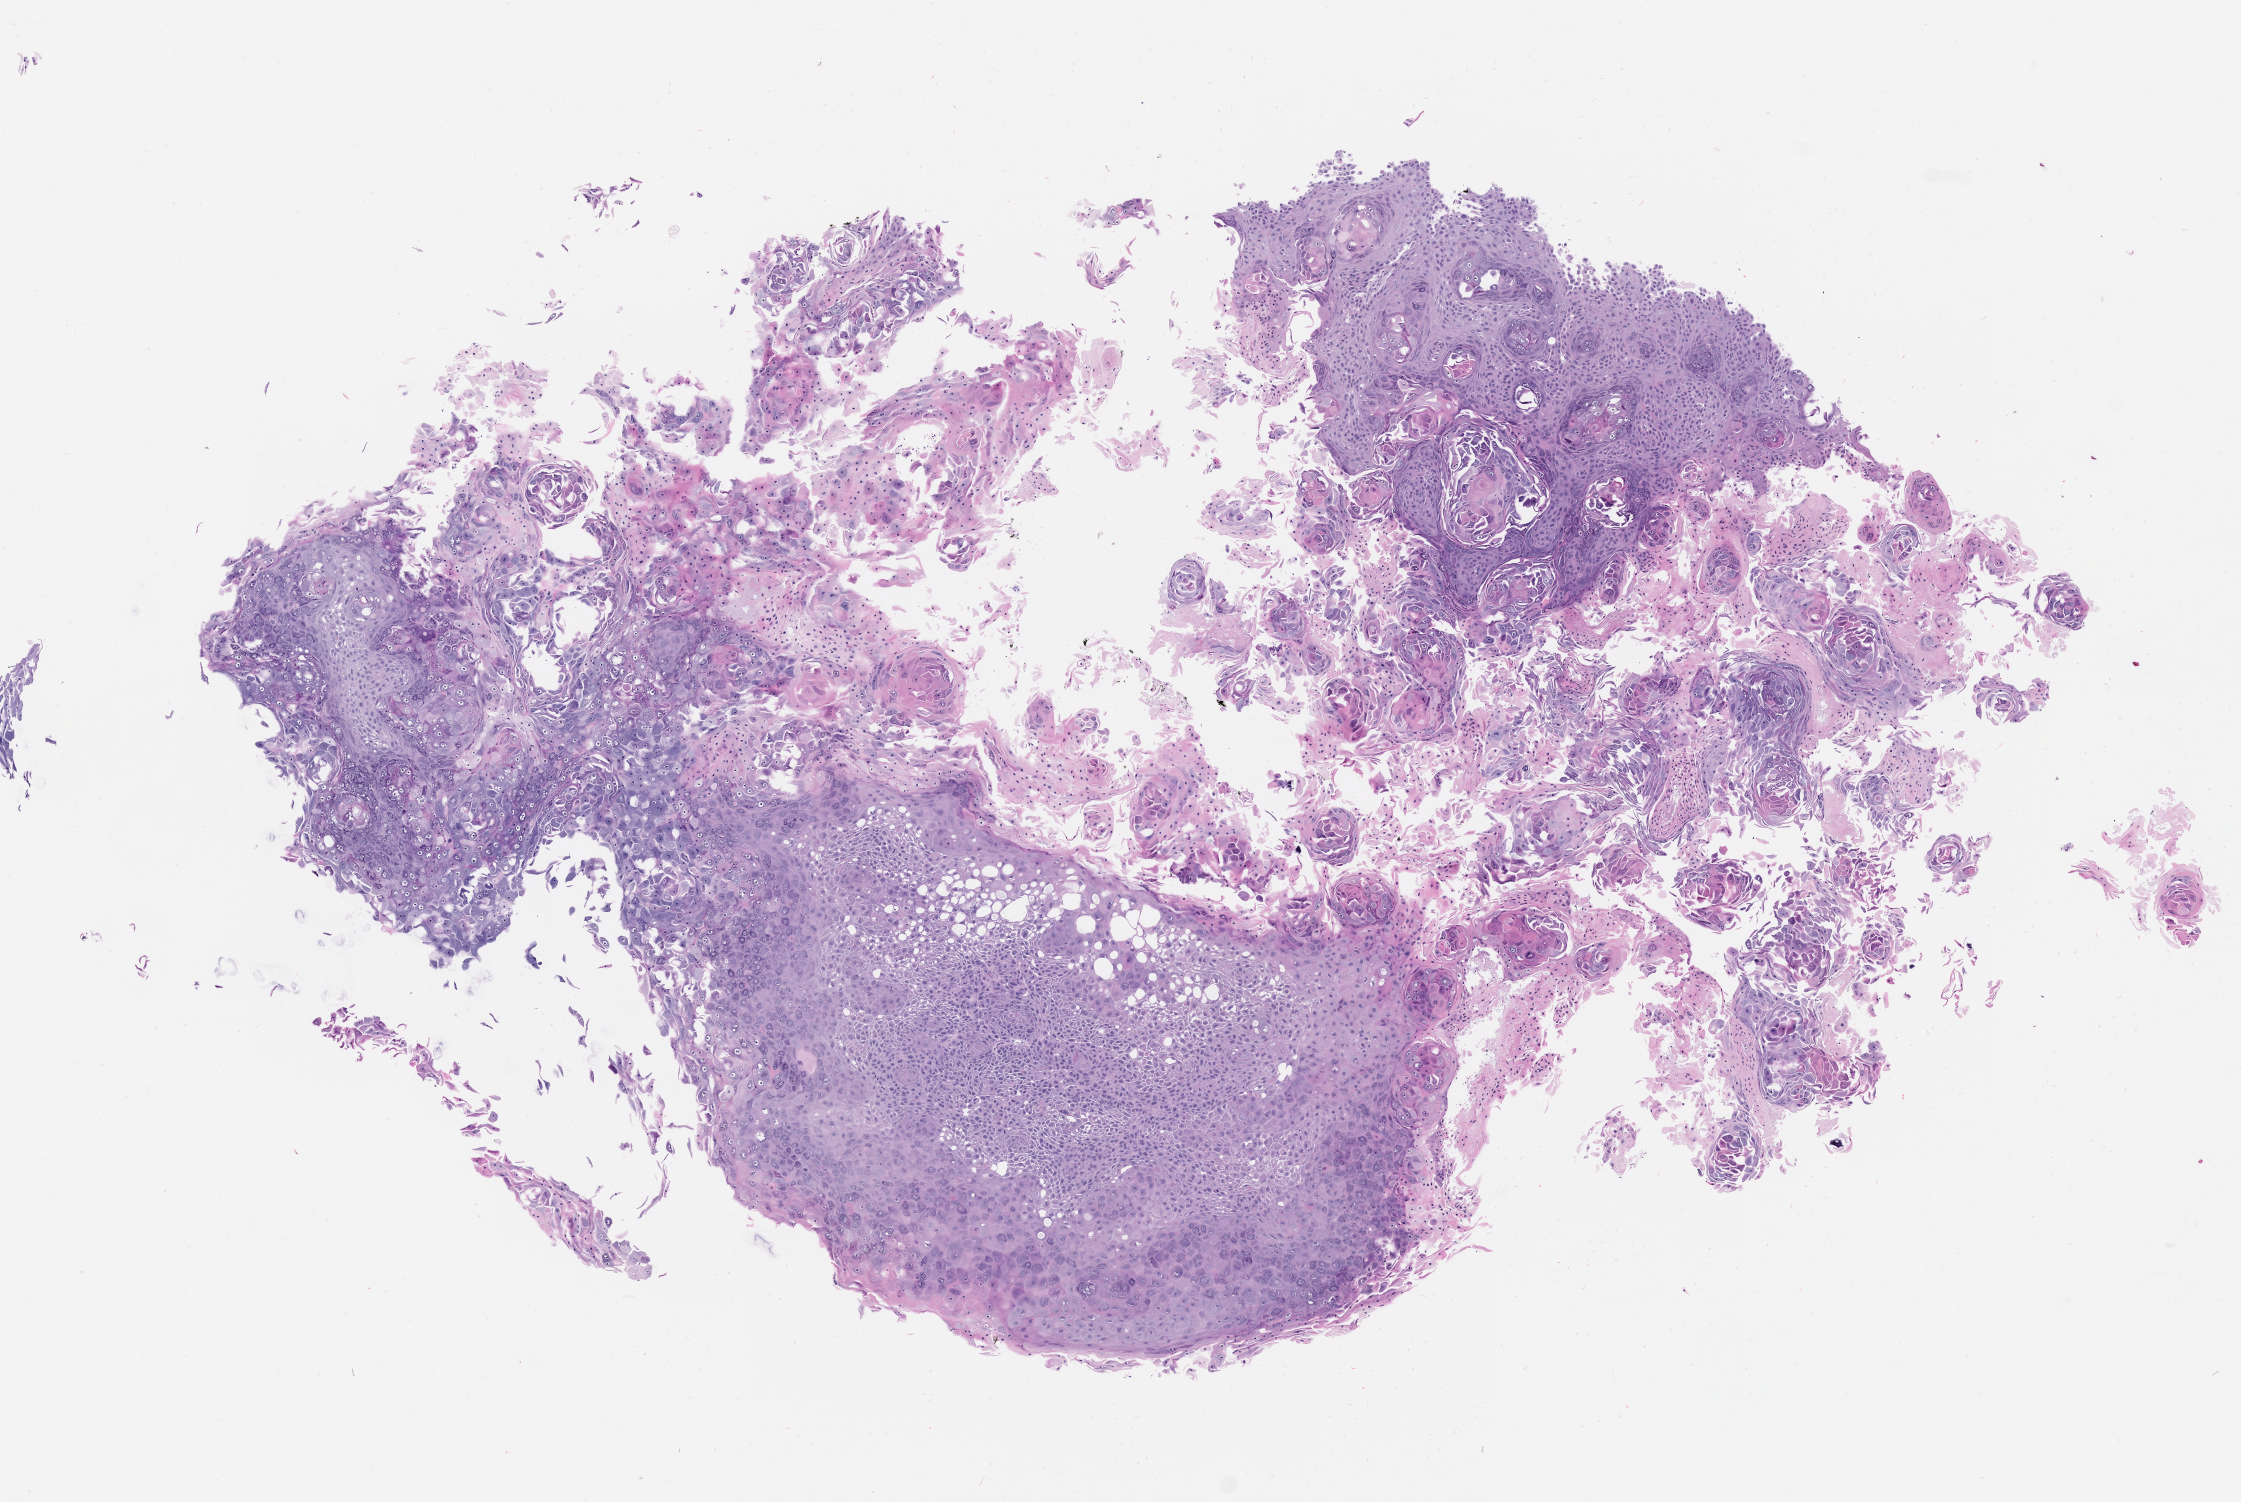
Haematoxylin and eosin whole-slide image of a patient-derived xenograft (PDX) tumor grown in a mouse, passage 2 — whole scanned area (about 9.0 x 6.0 mm) shown as a low-resolution overview, formalin-fixed, paraffin-embedded (FFPE) tissue, tumor site category: oral soft tissue.
• originating patient diagnosis: Head and Neck Squamous Cell Carcinoma